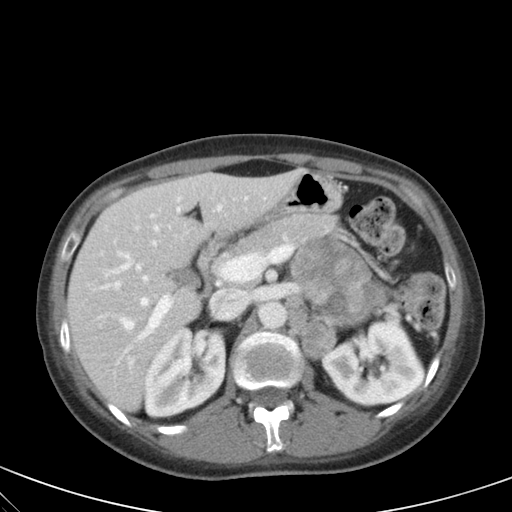
Contrast-enhanced abdominal CT, one axial slice. Slice 33 of 59 in the series (ordered by position). 120 kVp. Soft-tissue window (W 400 / L 40 HU). 512 × 512 image matrix, field of view 350 × 350 mm. Female patient, age 28 years. From the clinical record (not read from this slice): diagnosis: adrenocortical carcinoma; tumour side: left adrenal; tumour size at pathology: 7 cm; Ki-67 index: 40 %; stage (as recorded): 4.
Outlined on this slice (semi-automatically segmented with operator editing):
- mass: bounding box [x1, y1, x2, y2] px = [292, 242, 386, 325]